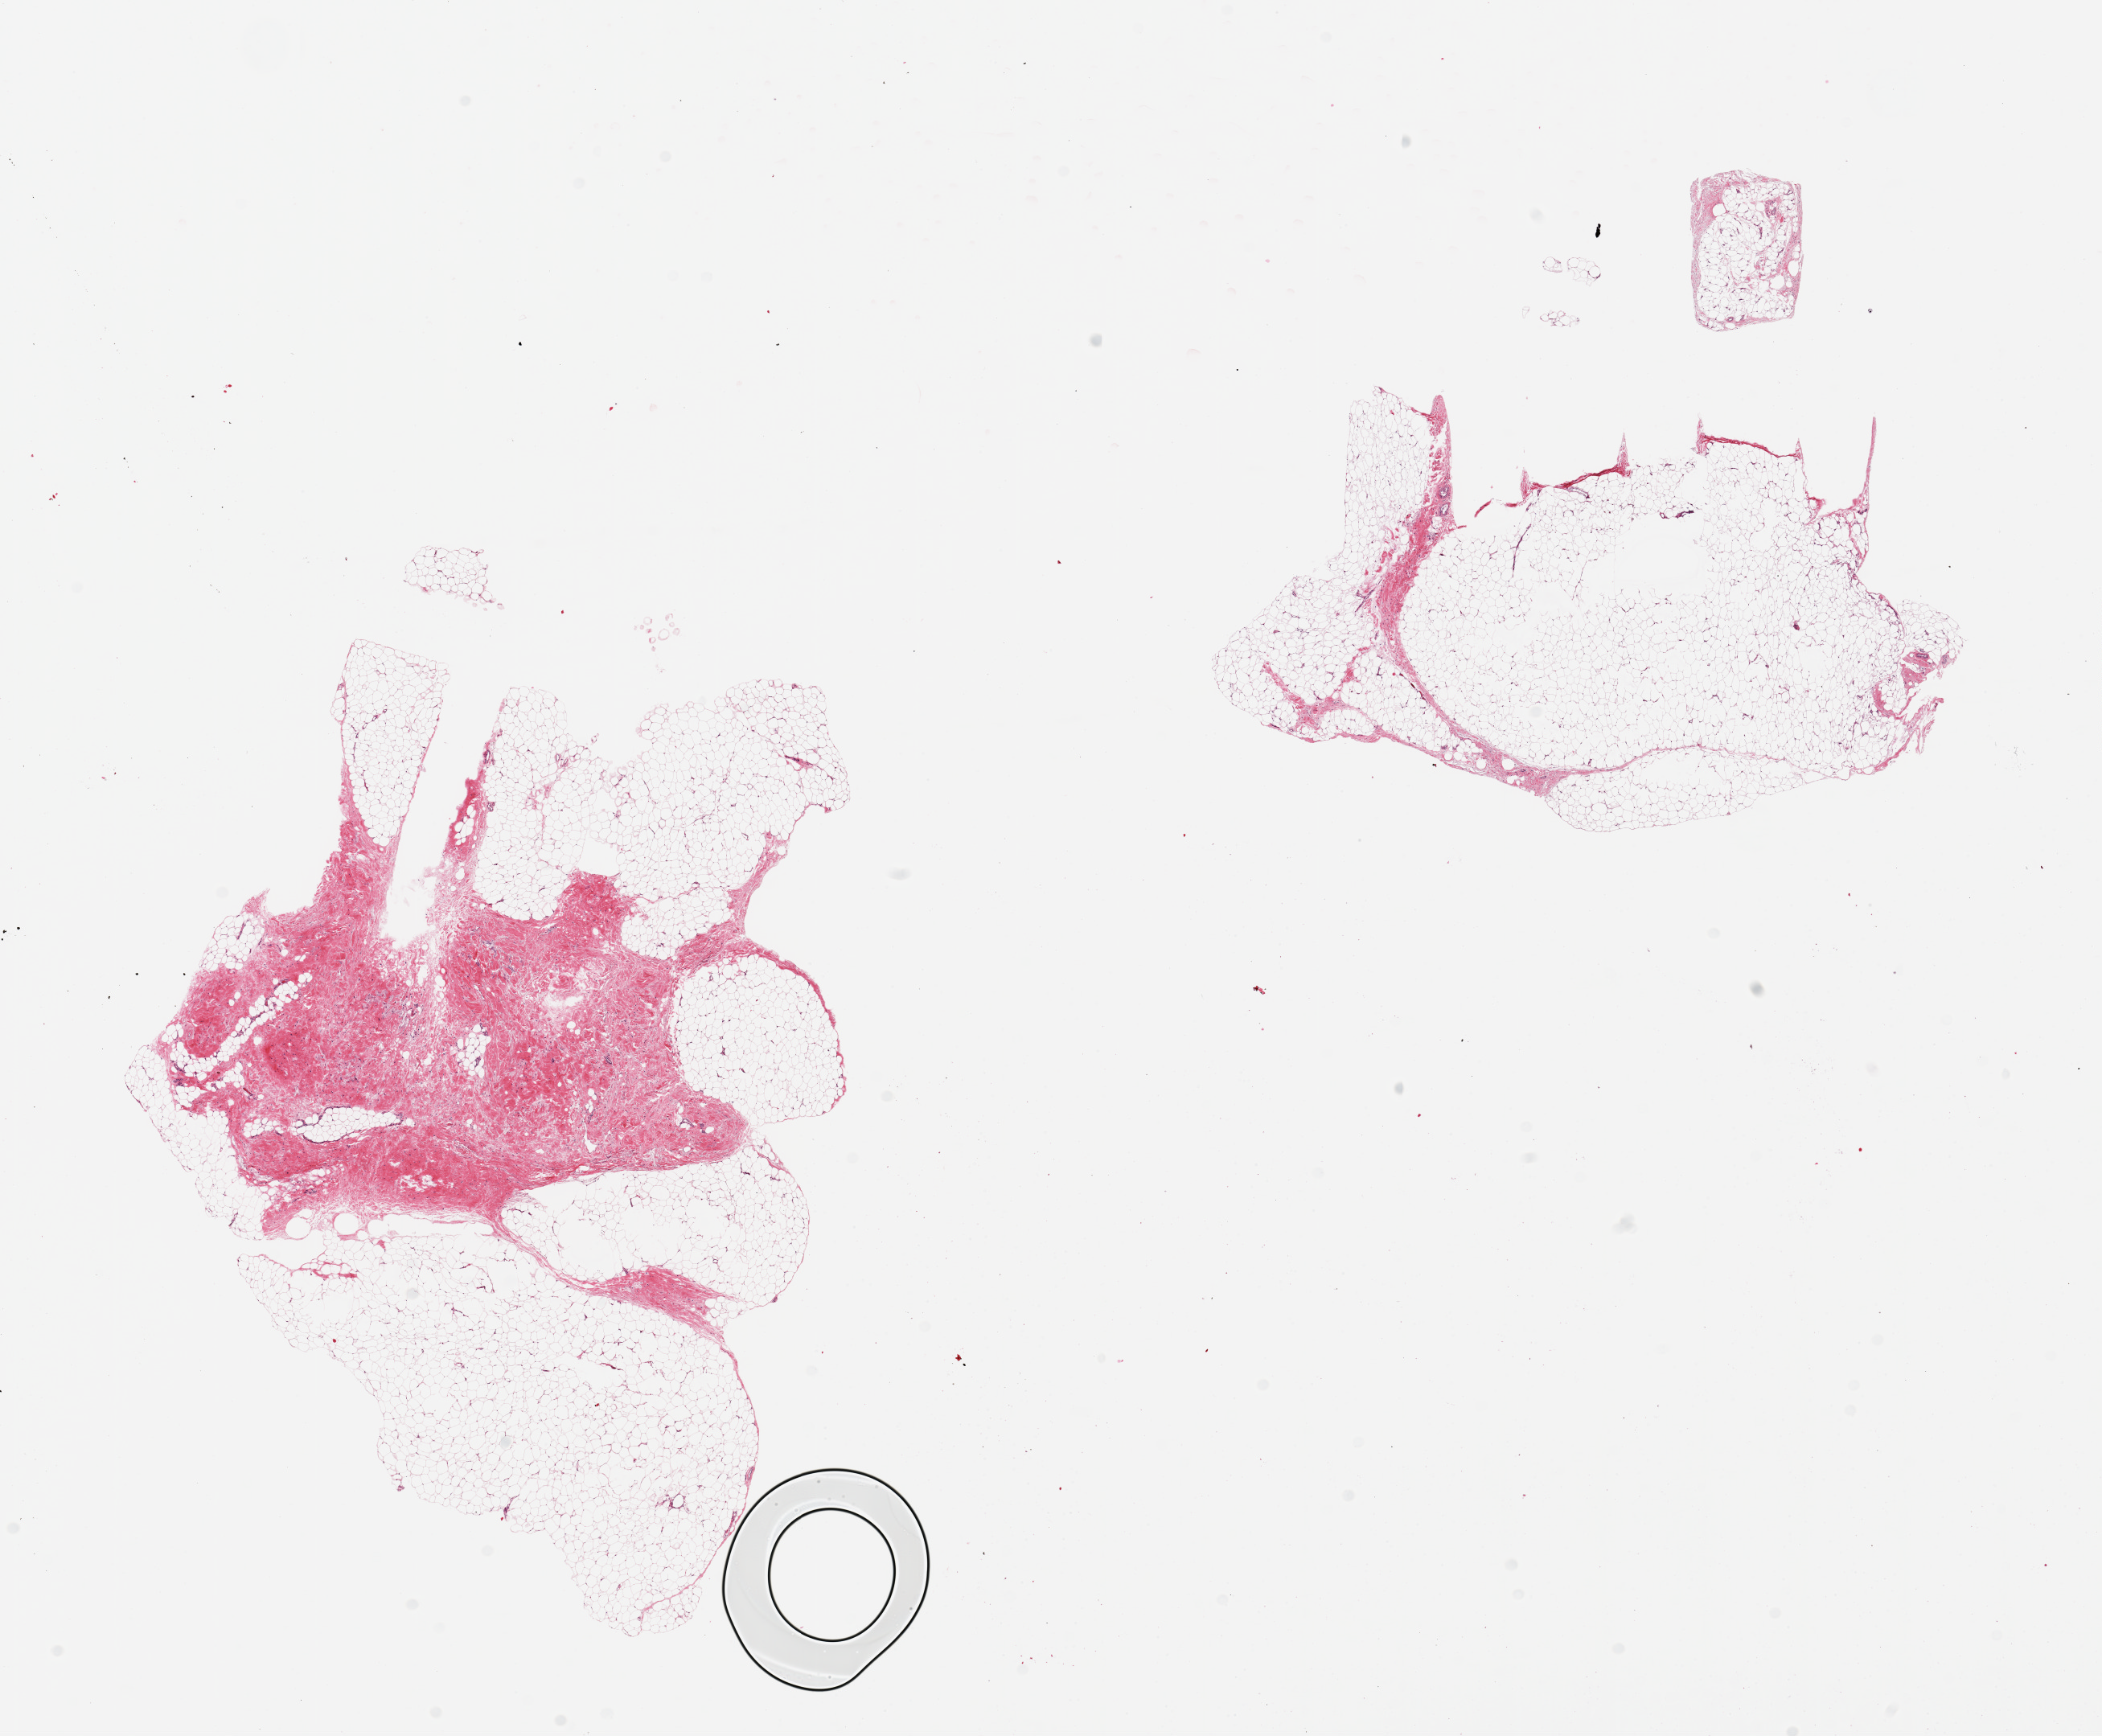
Whole-slide image, haematoxylin and eosin stain, brightfield — low-resolution overview of the scanned area, about 20.7 x 17.1 mm, PAXgene-fixed paraffin-embedded (PFPE) section, sampled site (target tissue): adipose tissue, donor tissue sample. Donor: female.
Pathologist's review note for this sample: 2 pieces; one contains 50% fibrous tissue.